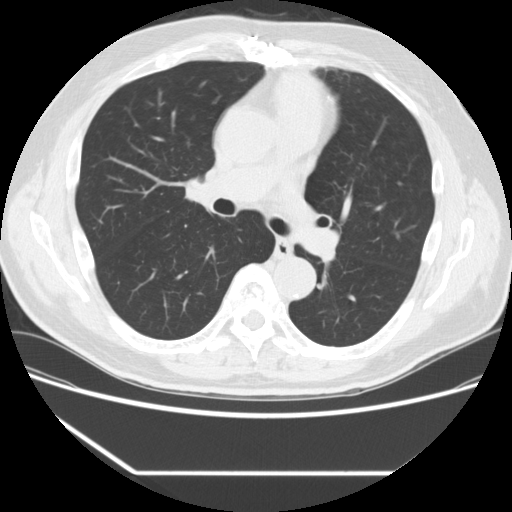
Chest CT (low-dose screening protocol), one axial image, first (baseline) screen, lung window (W 1500 / L -600 HU), 512 × 512 image matrix. Male participant, aged 66 years at enrolment. Former smoker at enrolment.
Lesion marked by an expert reader, bounding box (x1, y1, x2, y2) in pixels: (327, 170, 363, 203). Reader record for this screening exam (exam-level; its link to the box is not recorded): non-calcified nodule or mass ≥4 mm, right lower lobe, 4 × 4 mm, smooth margins, soft tissue attenuation. Note: the box lies in the patient's left hemithorax on this image, whereas the reader's record names the right lung; they may be different findings. Lung cancer was diagnosed 792 days after this screen (after the third annual screen): squamous cell carcinoma, NOS, left upper lobe, poorly differentiated (G3), stage IA (AJCC 6th edition), 27 mm at pathology.